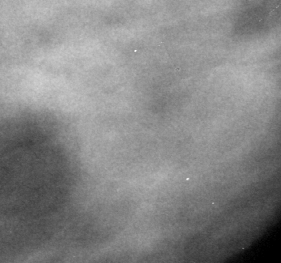
Cropped region of a digitized screen-film mammogram centred on a radiologist-marked abnormality, left breast, CC view.
- Finding: mass, shape irregular, margins obscured / ill defined; BI-RADS assessment category 3; subtlety rating 2 on a 1 (subtle) to 5 (obvious) scale; pathology result (as recorded, not read from the image): malignant.